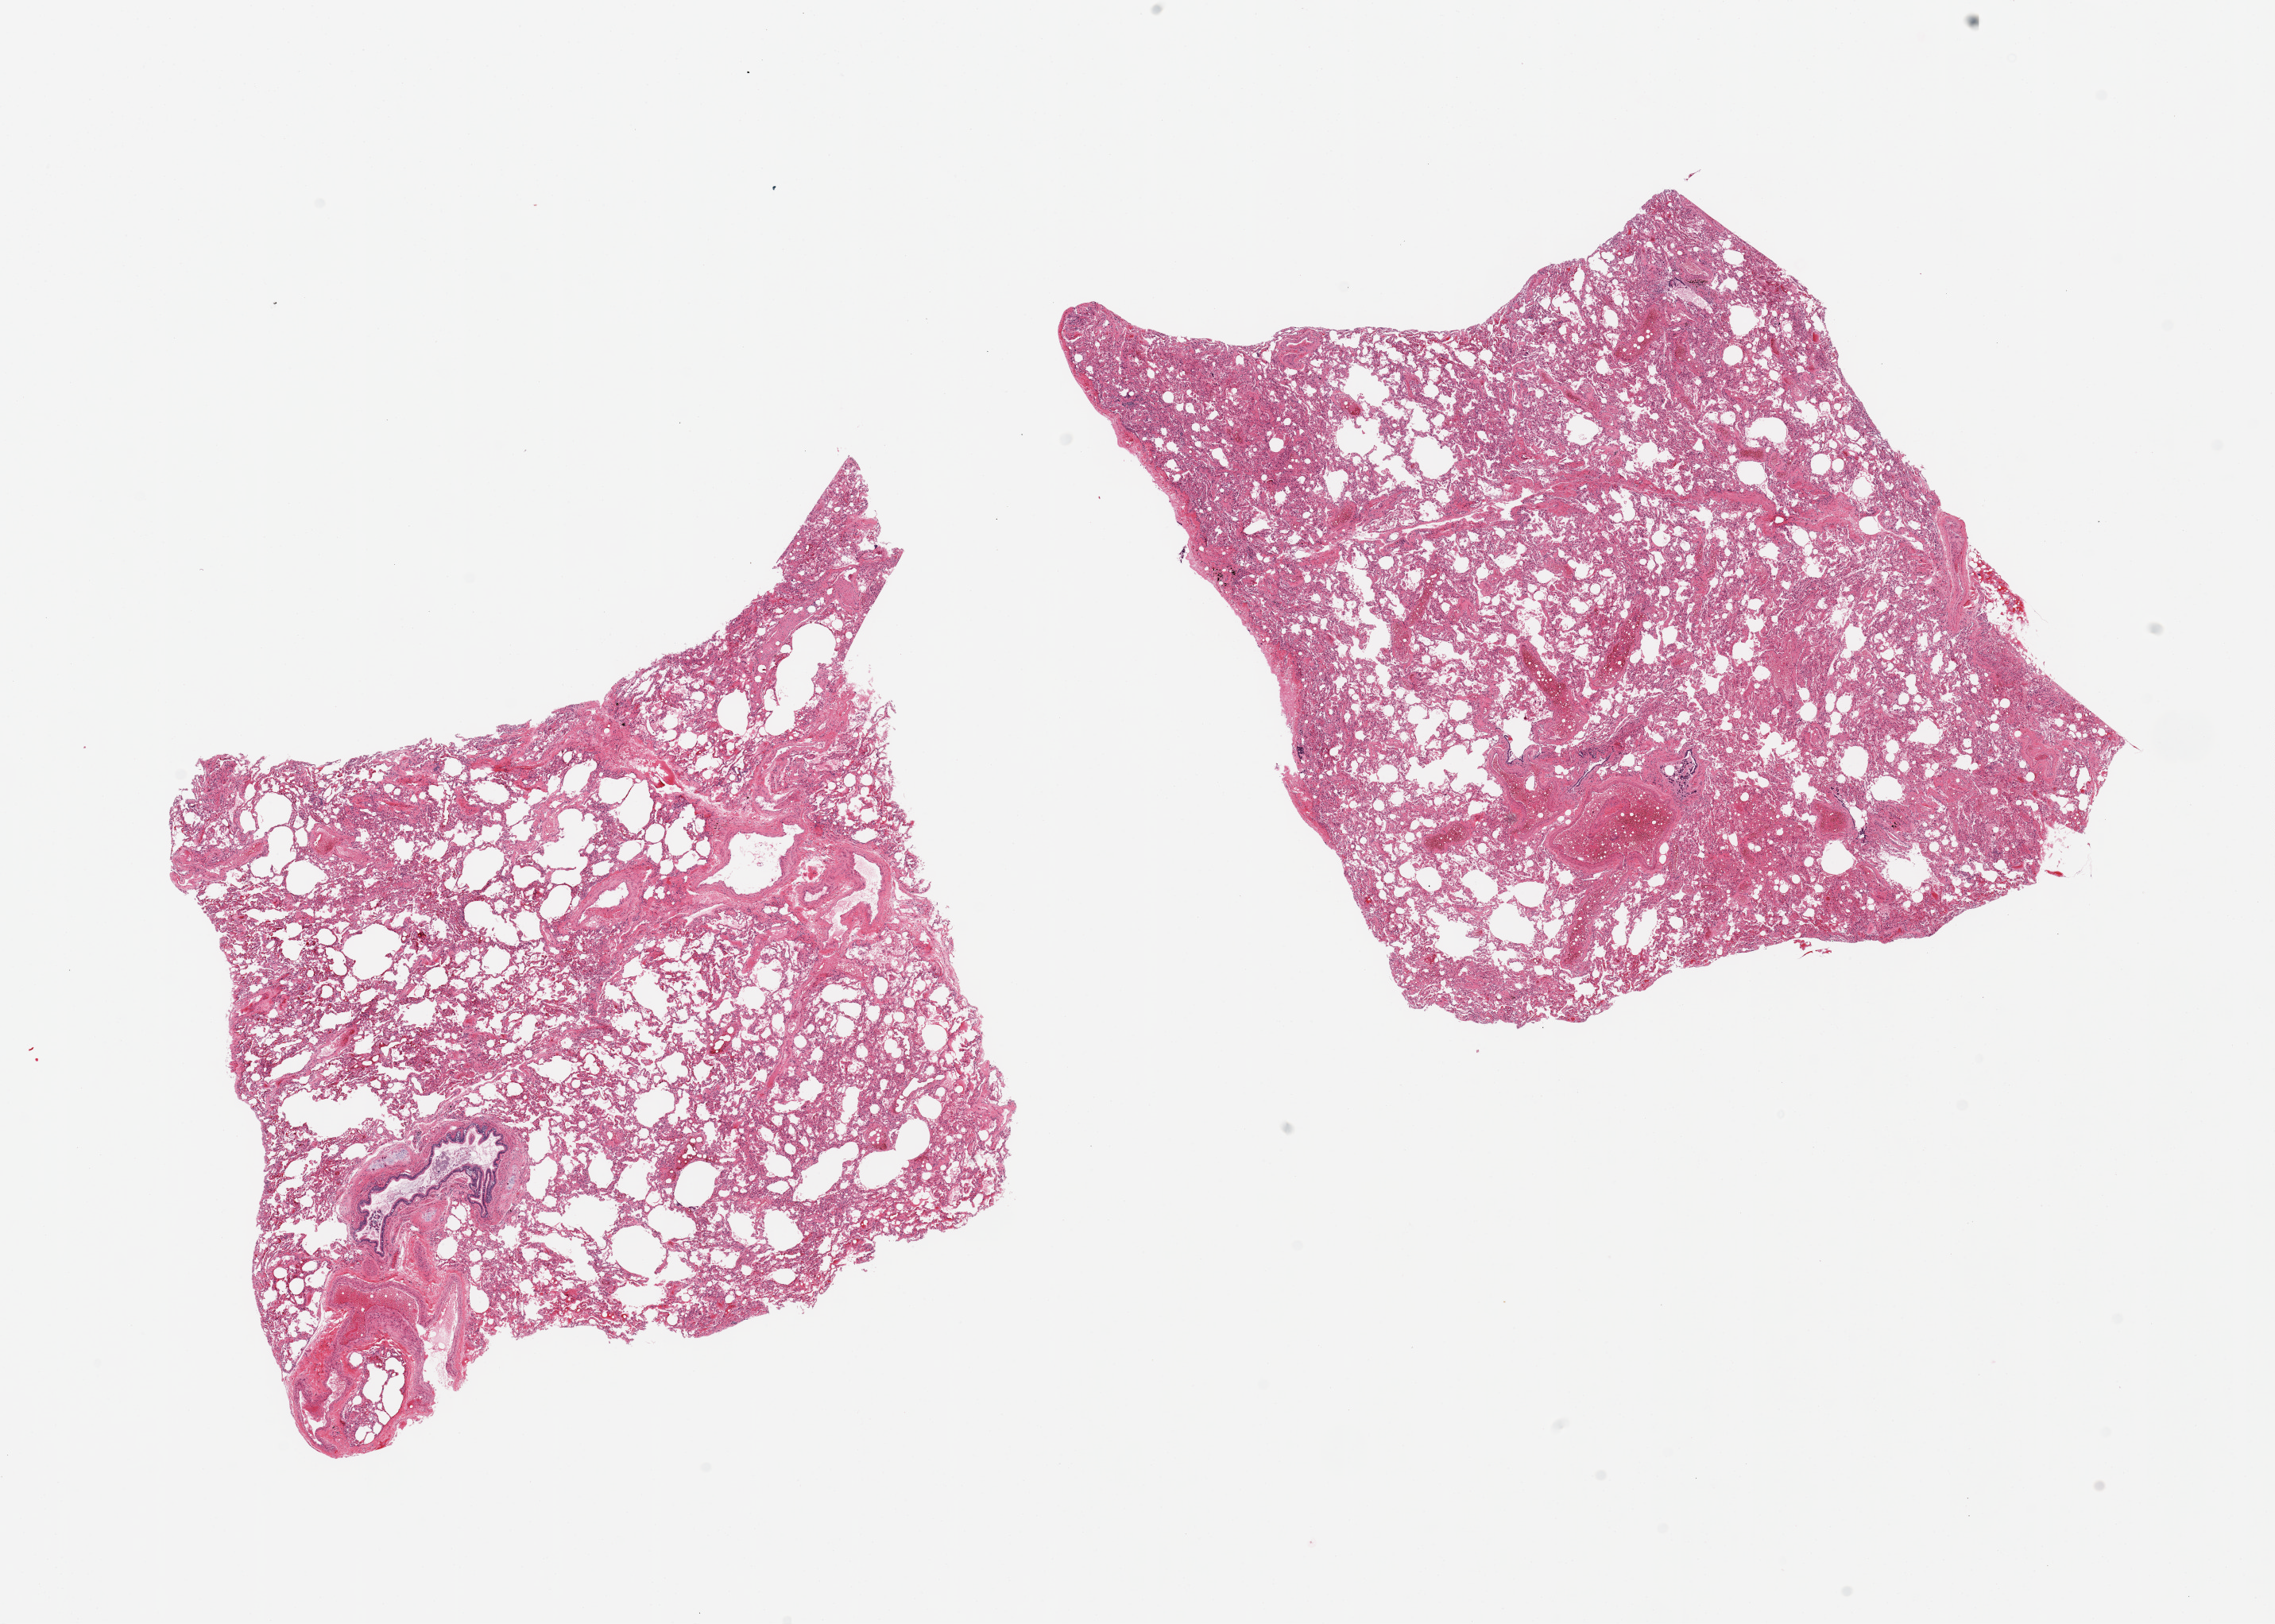
Hematoxylin and eosin (H&E) whole-slide image, brightfield — whole scanned area (about 22.6 x 16.2 mm) shown as a low-resolution overview, PAXgene-fixed paraffin-embedded (PFPE) section, sampled site (target tissue): lung, tissue donor sample. Donor sex: female.
Reviewer comment on this tissue sample: 2 pieces; emphysema; mild fibrosis; congestion; bronchus with cartilage in 1 piece.